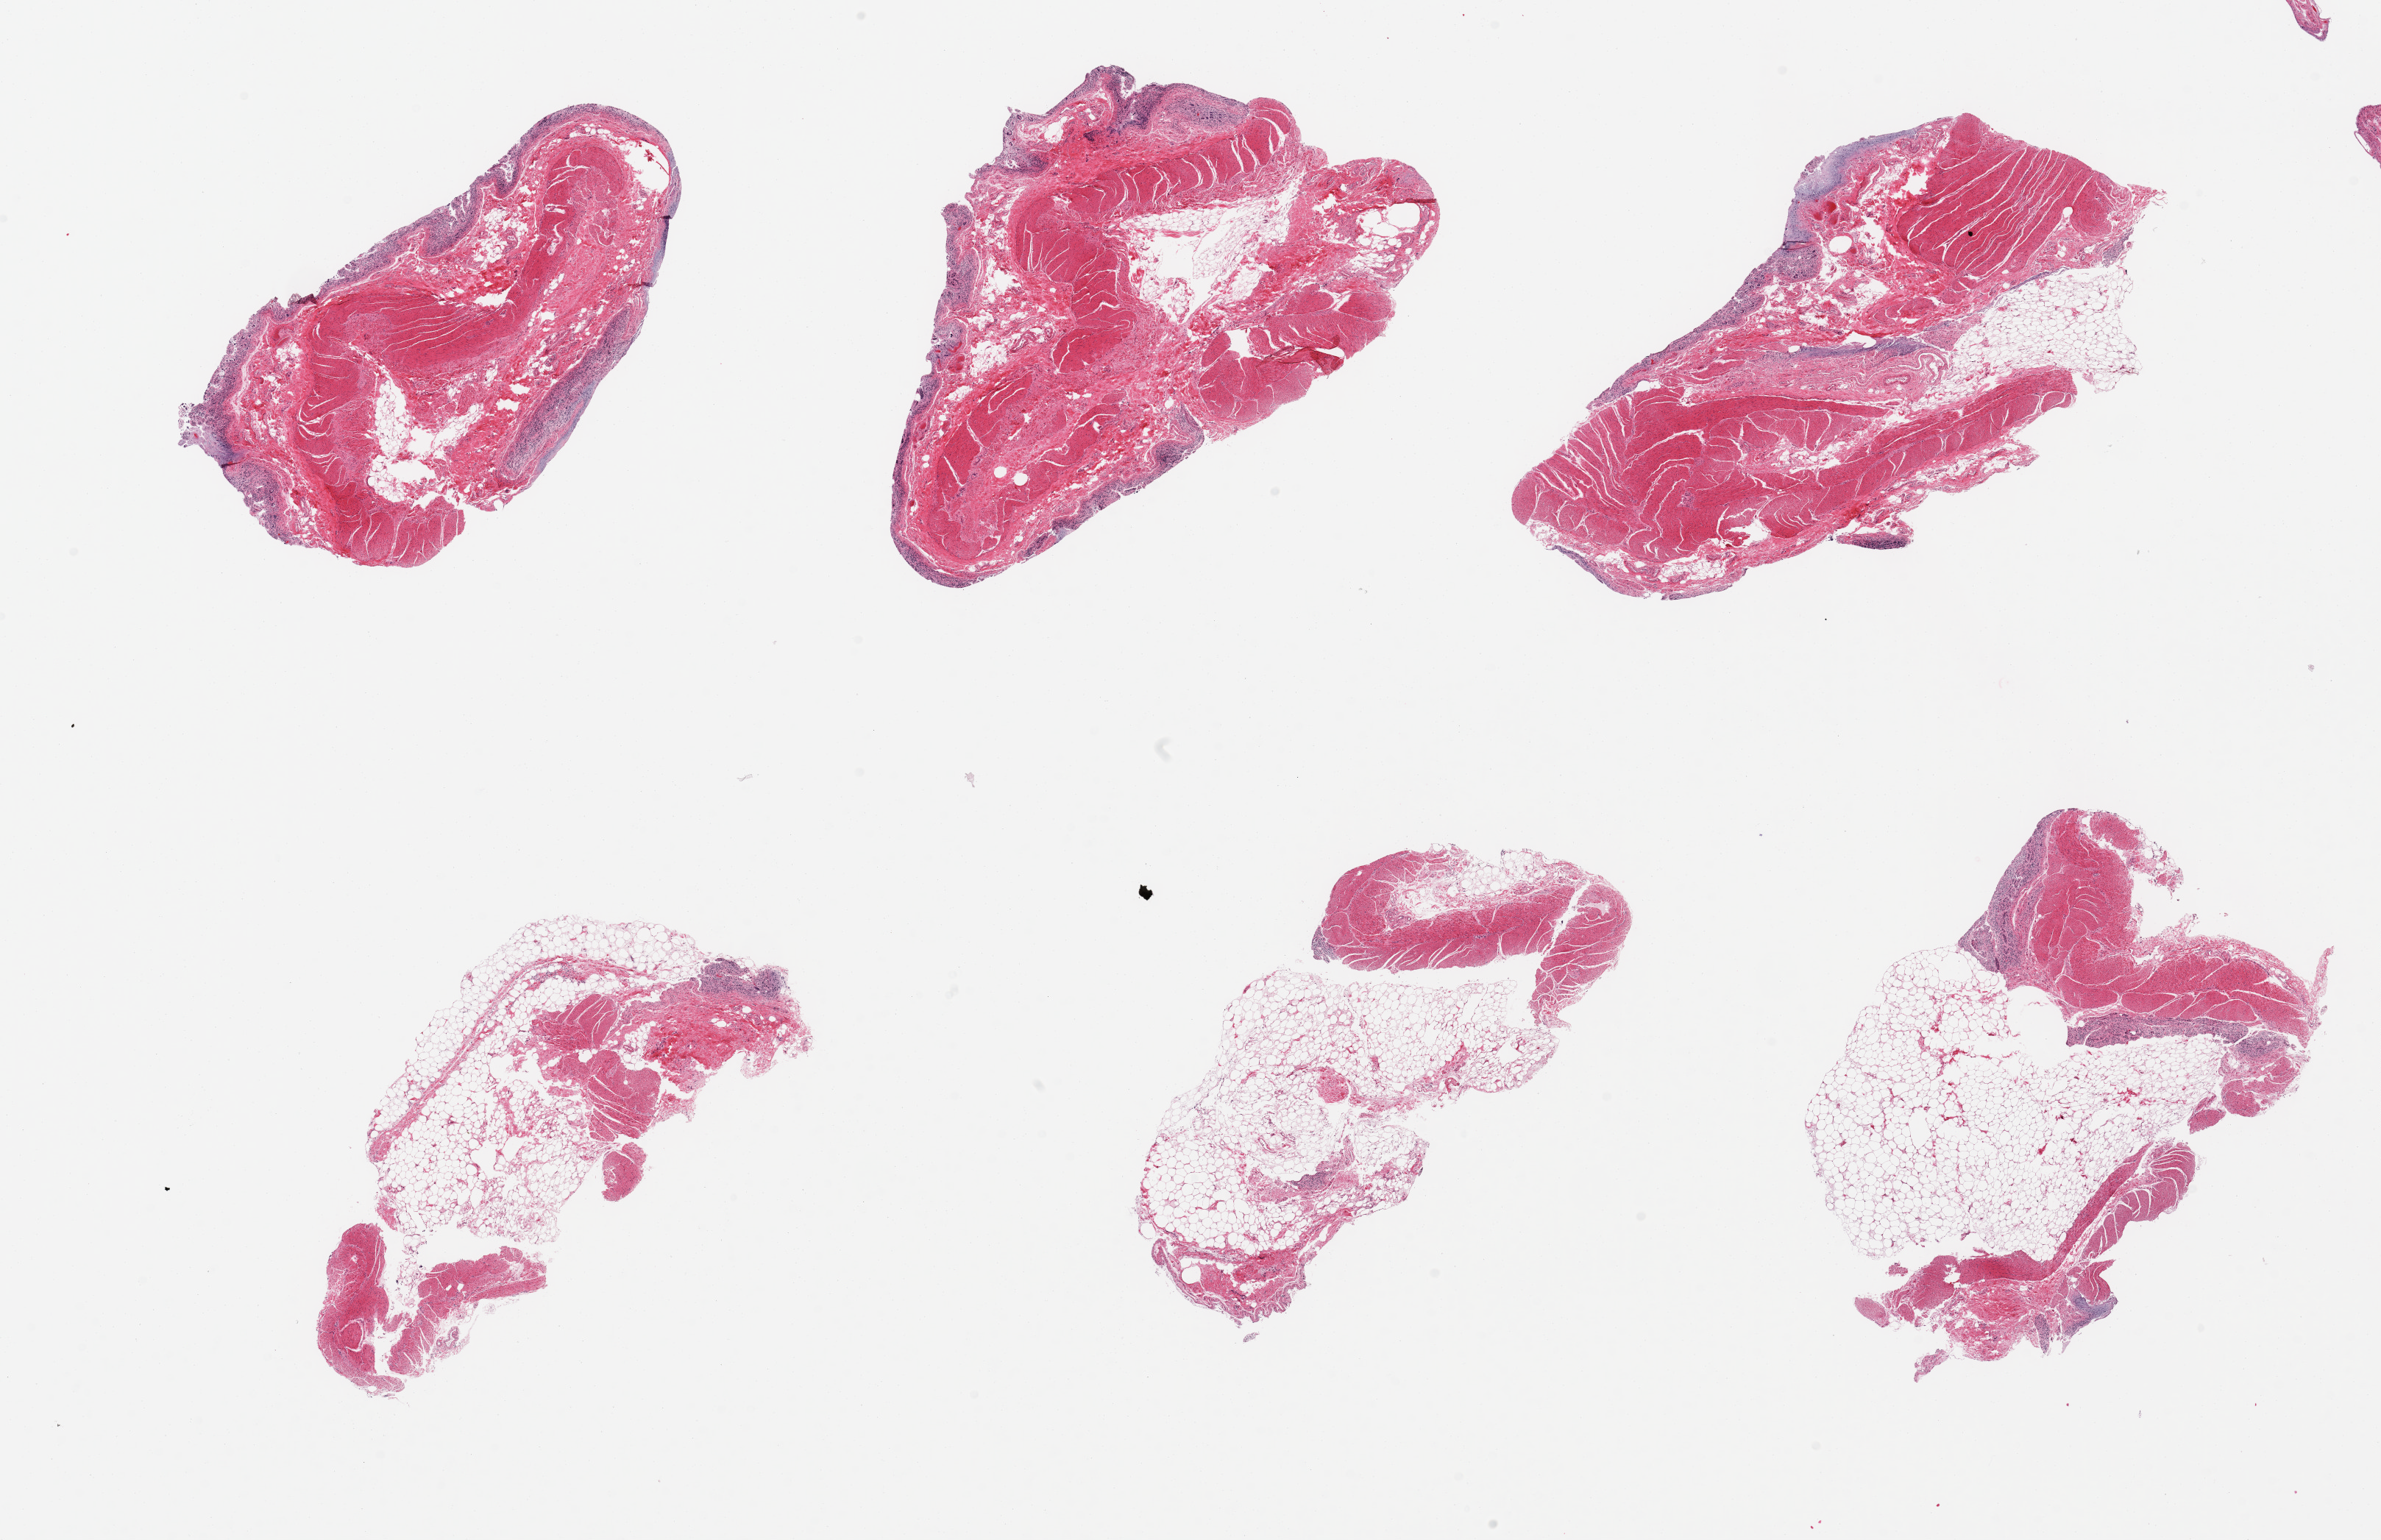
Digitized haematoxylin and eosin-stained section, whole scanned area (about 25.6 x 16.6 mm) shown as a low-resolution overview, PAXgene-fixed, paraffin-embedded tissue, target tissue: ileum, donor tissue sample. Male donor.
Reviewer comment on this tissue sample: 6 pieces, No target lymphoid aggregates, ~70% muscularis/adipose tissue.